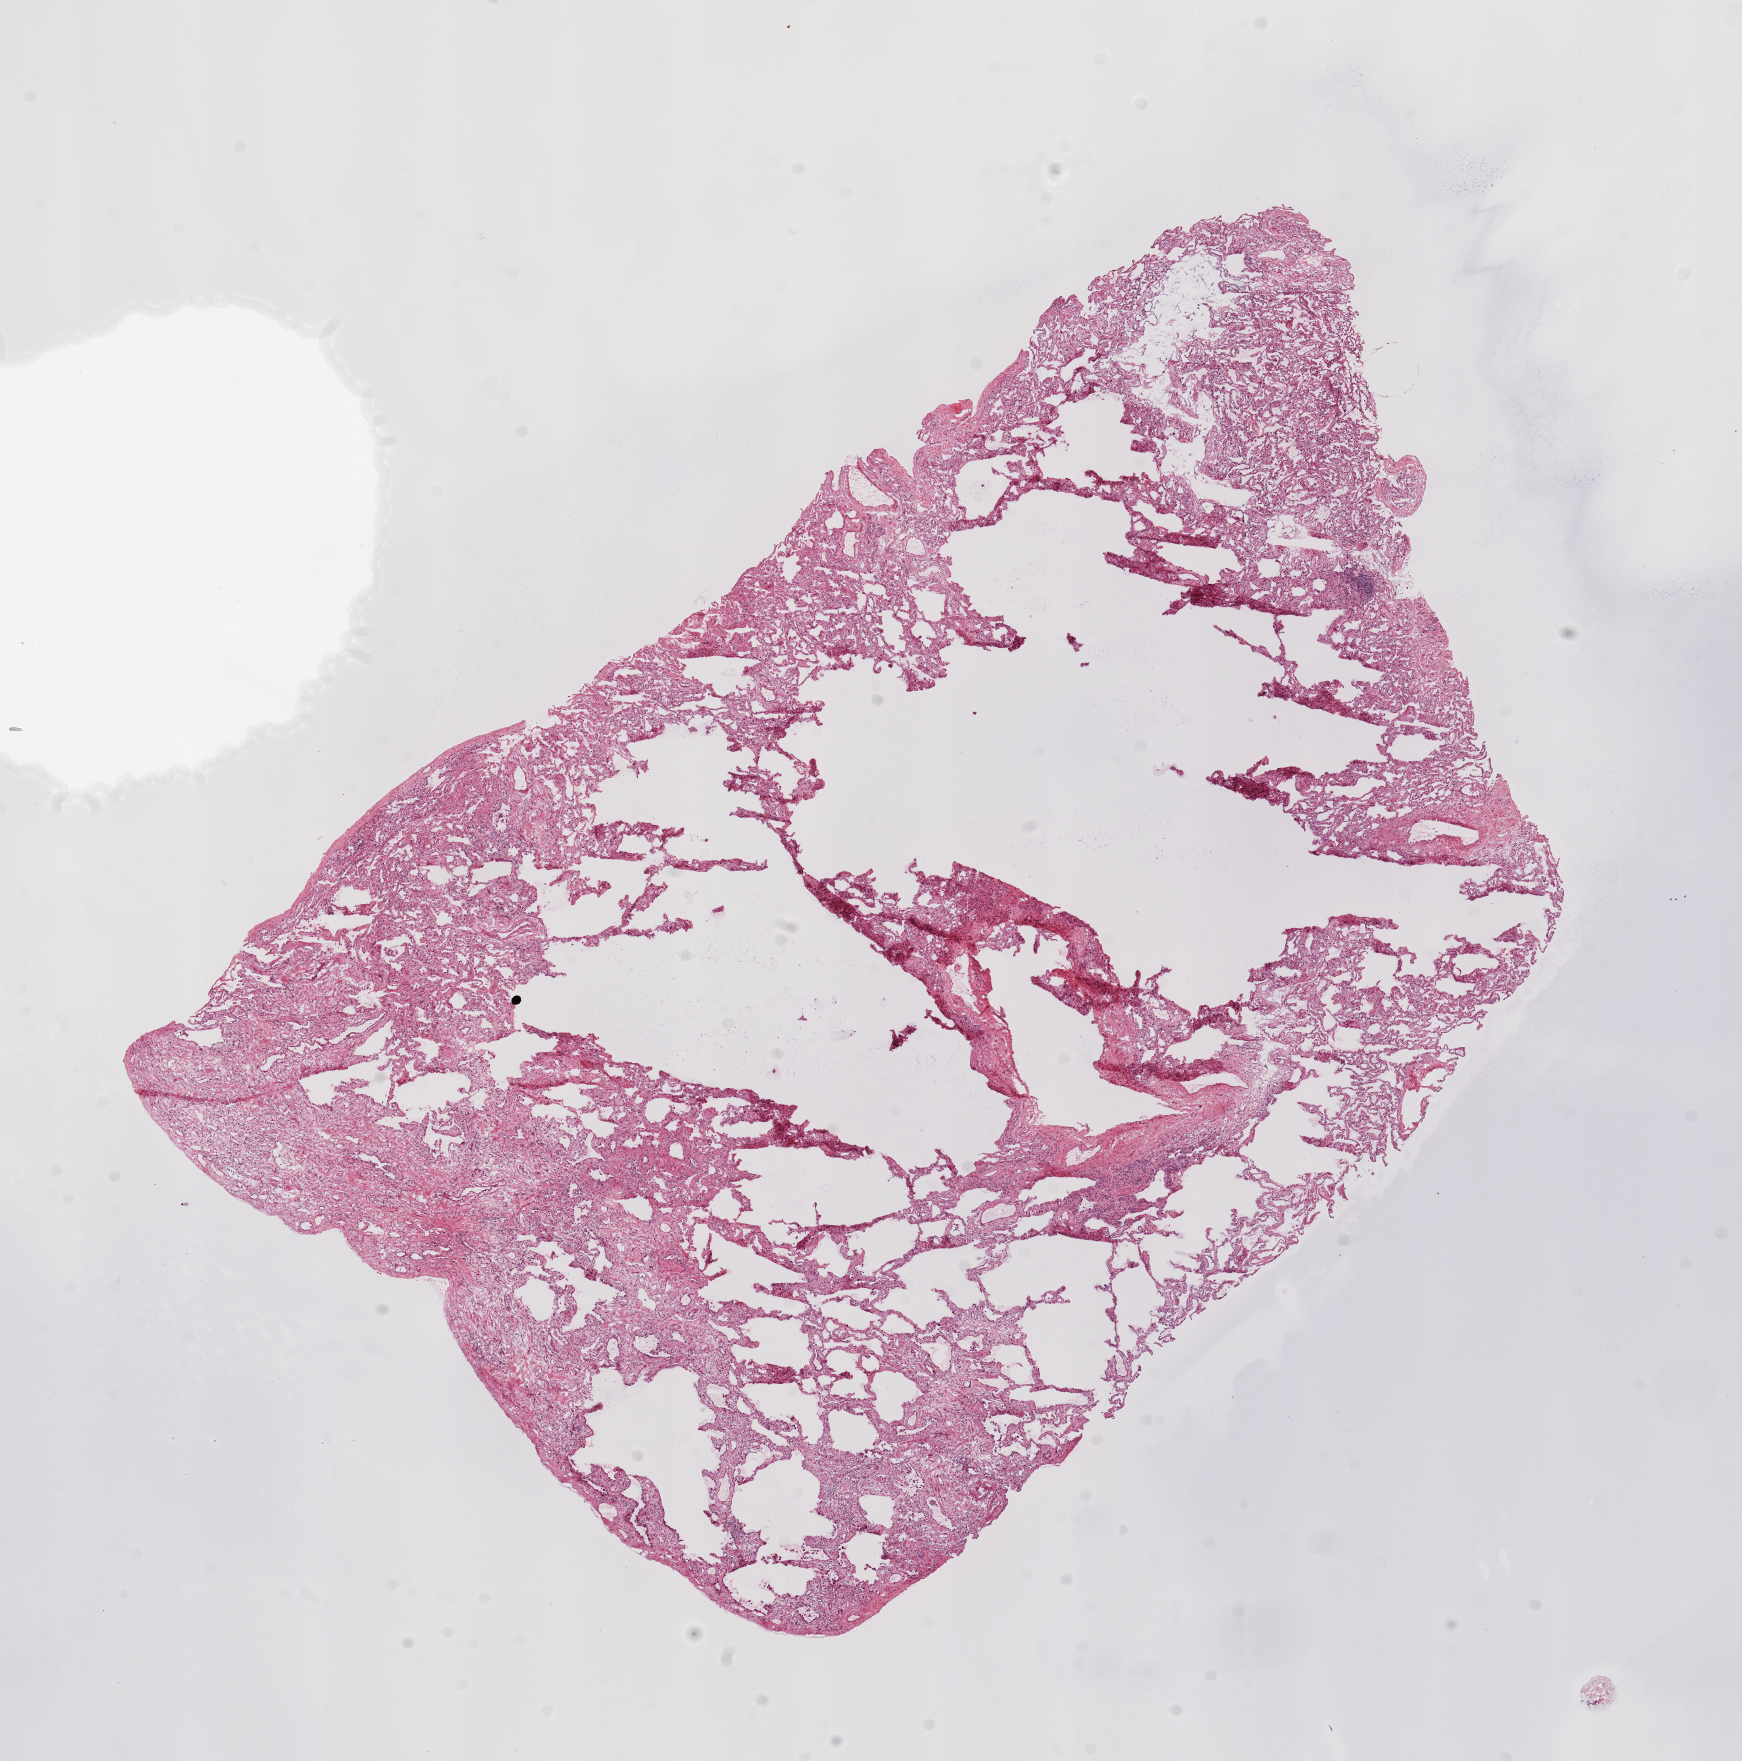
Digitized H&E-stained tissue section (whole slide), shown as a low-resolution overview of the whole scanned area (about 13.8 x 13.9 mm), normal (non-tumour) tissue sample, lung. Female, 80 y/o.
* this section: normal (non-tumour) tissue from the same patient
* patient diagnosis: Adenocarcinoma, NOS